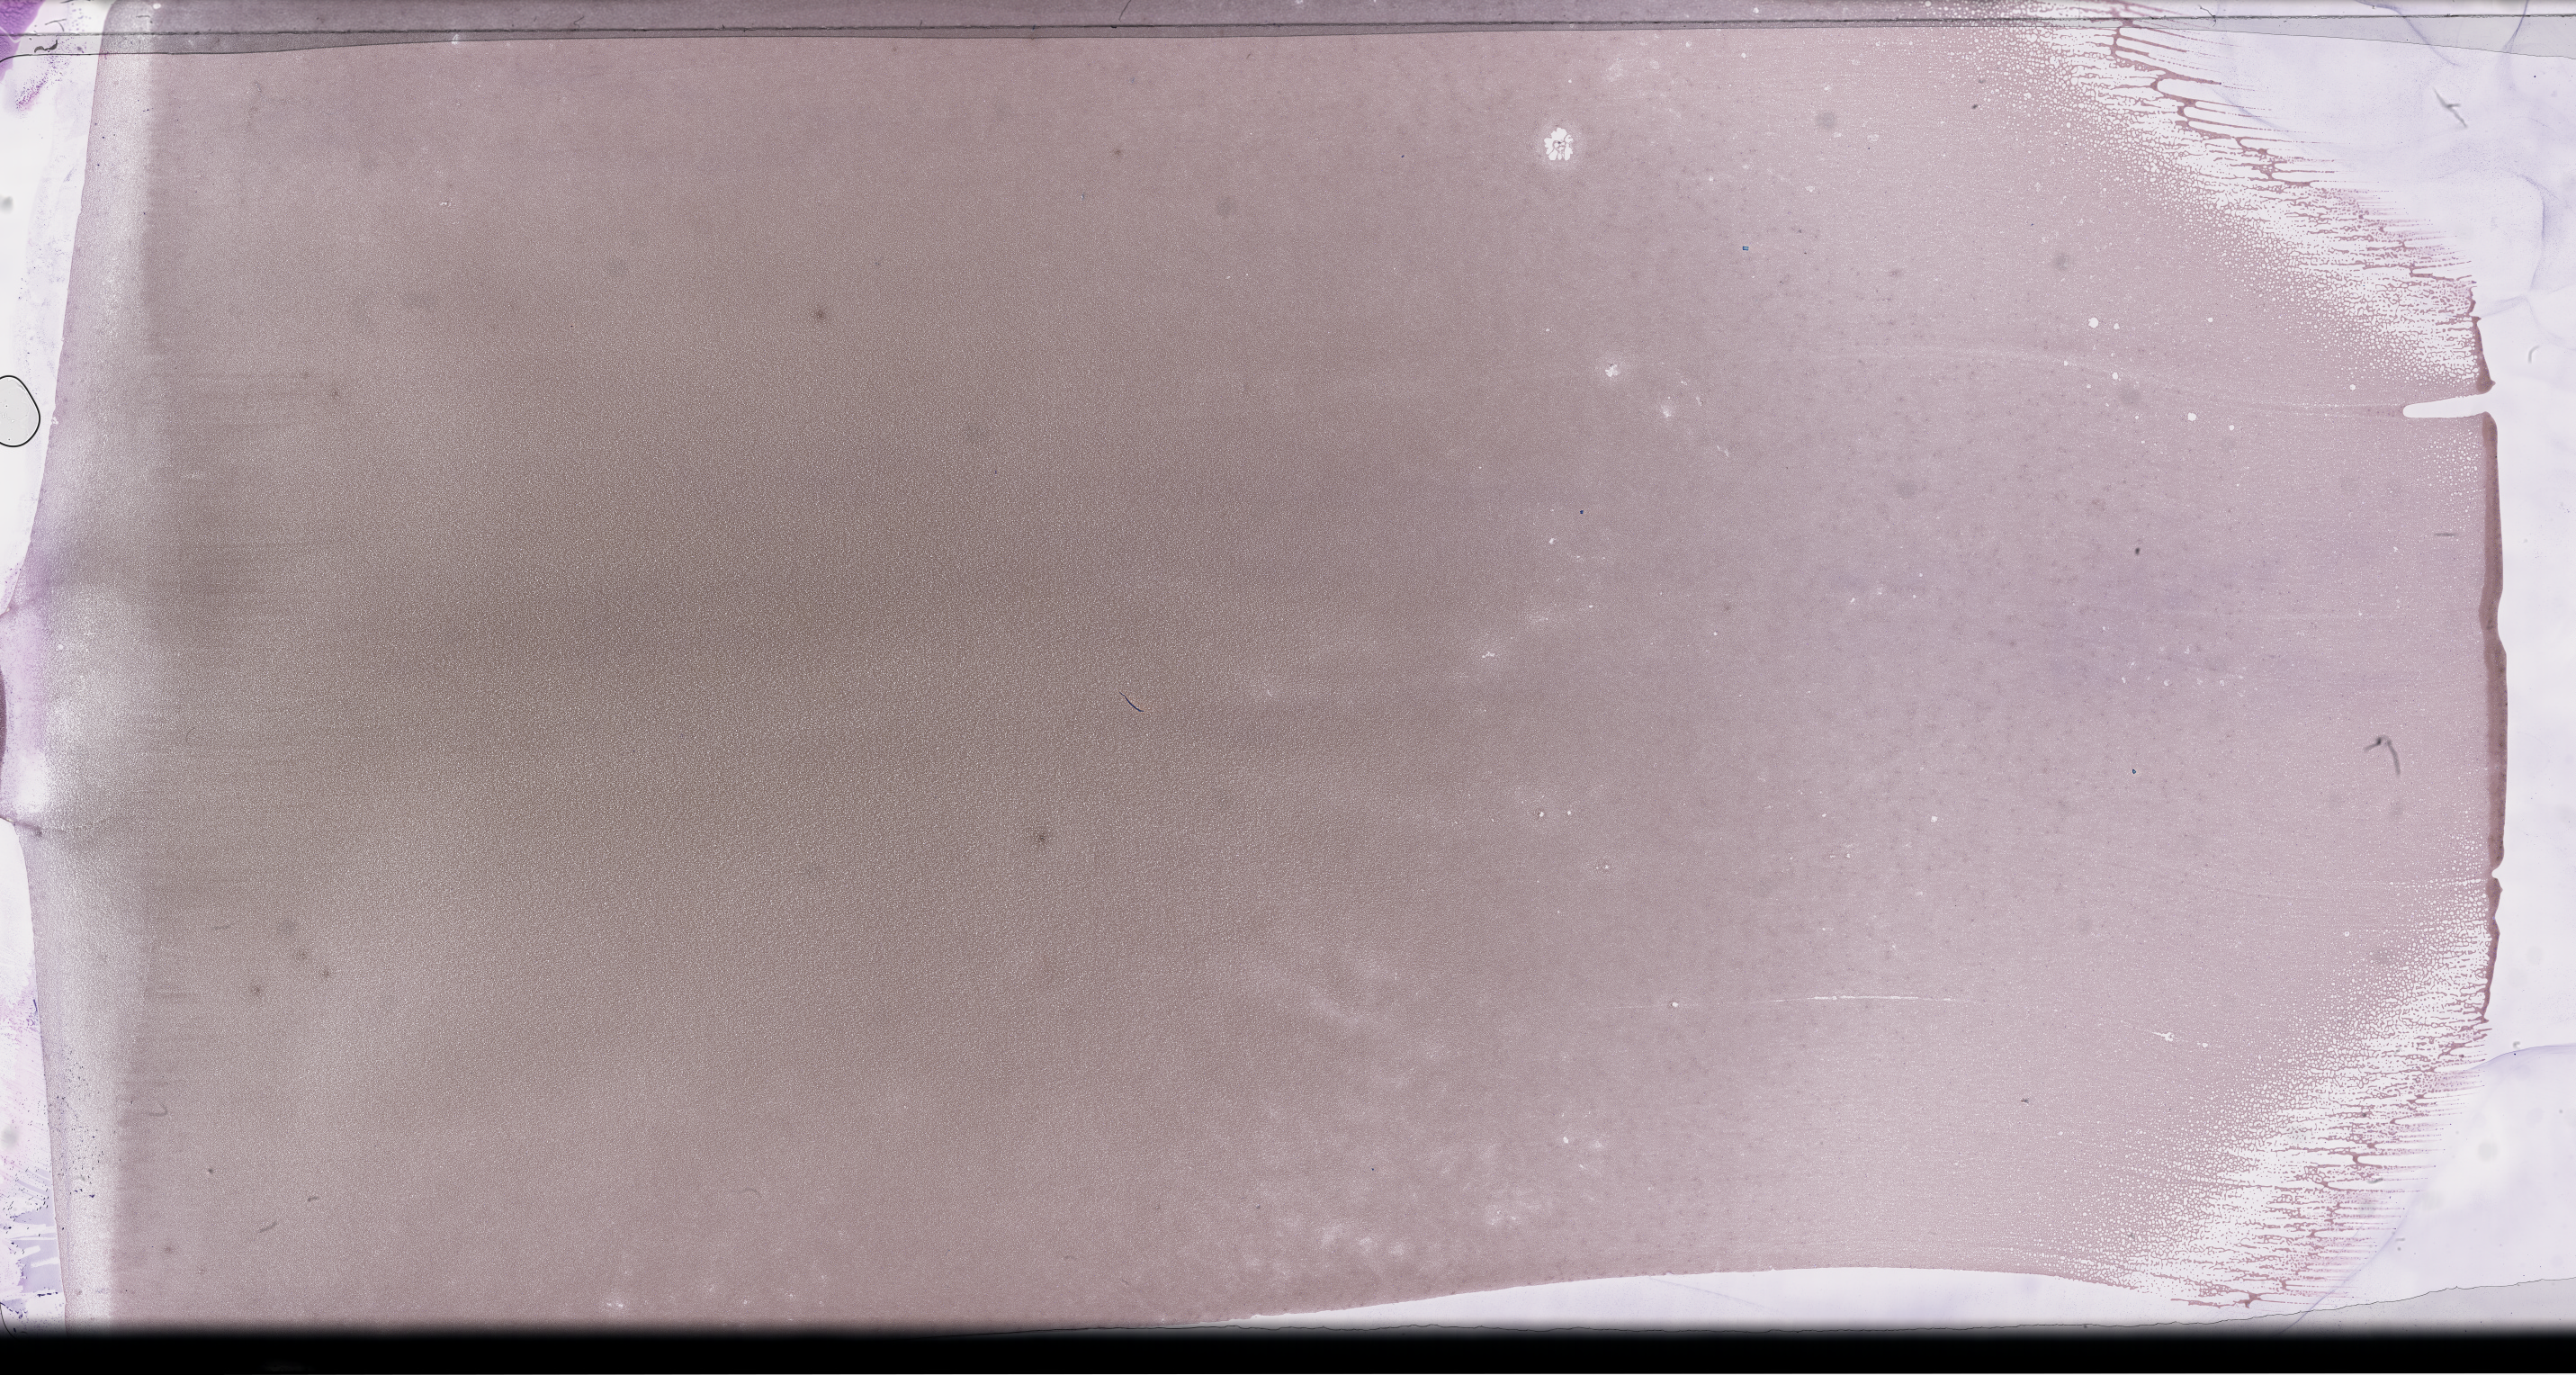
Whole-slide image of a whole blood smear, Wright-Giemsa stain, whole scanned area (about 46.2 x 24.7 mm) shown as a low-resolution overview. EDTA-anticoagulated smear. Collected on treatment. Patient sex: male.
Patient diagnosis: Plasma Cell Myeloma.